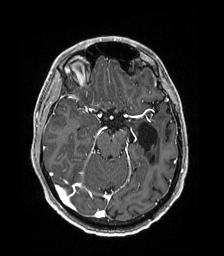
Brain MRI from a brain-tumour surgery series, one axial slice. Position 114 of 192 along the scan axis. T1-weighted post-contrast. 1 mm slice thickness. 224 × 256 image matrix. From the clinical record (not read from this slice): histopathology: Low grade glioma; IDH mutation: no; tumour location: Left Parieto-Occipital Intraventricular.
Outlined on this slice (manually delineated by an expert):
- previous resection cavity: bounding box [x1, y1, x2, y2] px = [138, 123, 158, 164]